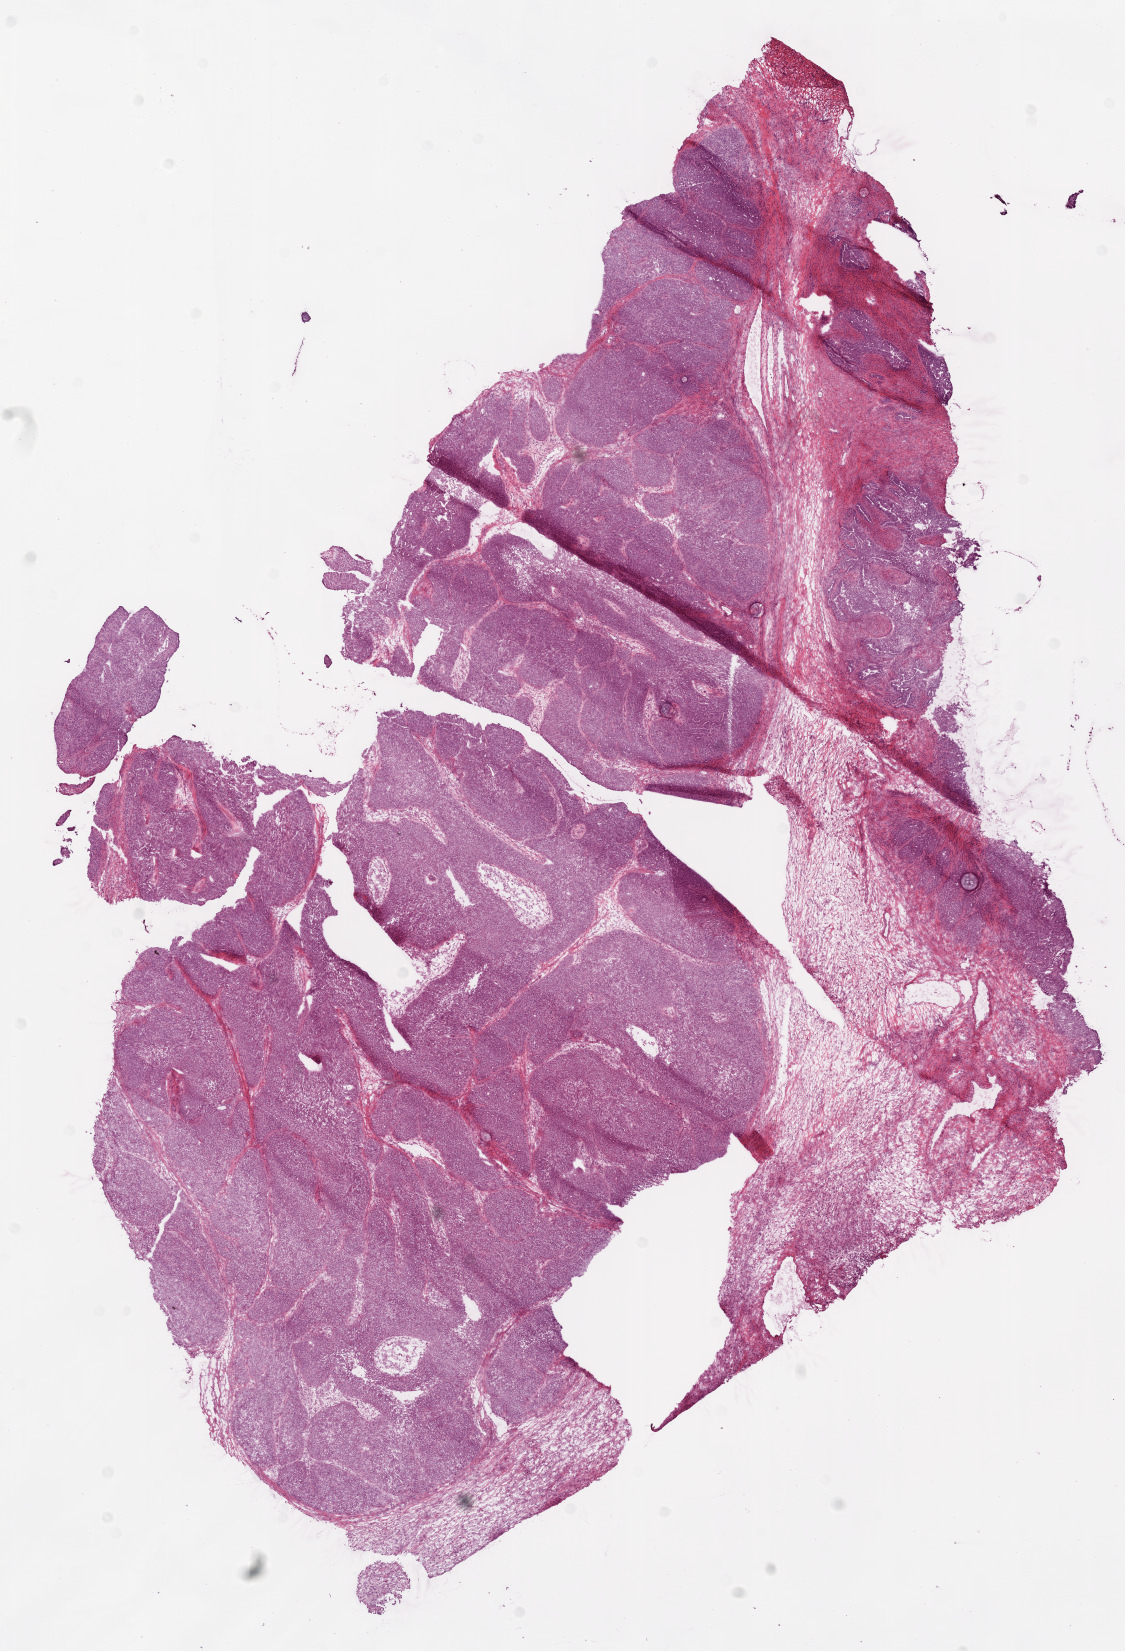
H&E-stained whole-slide image — shown as a low-resolution overview of the whole scanned area (about 9.0 x 13.2 mm, slide scanned at 20x), frozen section, ovary, primary tumour sample. Patient: female, age at initial diagnosis 62 years. Composition of this section per pathologist review: tumour cells 90%, tumour nuclei 90%.
Diagnosis: Serous cystadenocarcinoma, NOS.